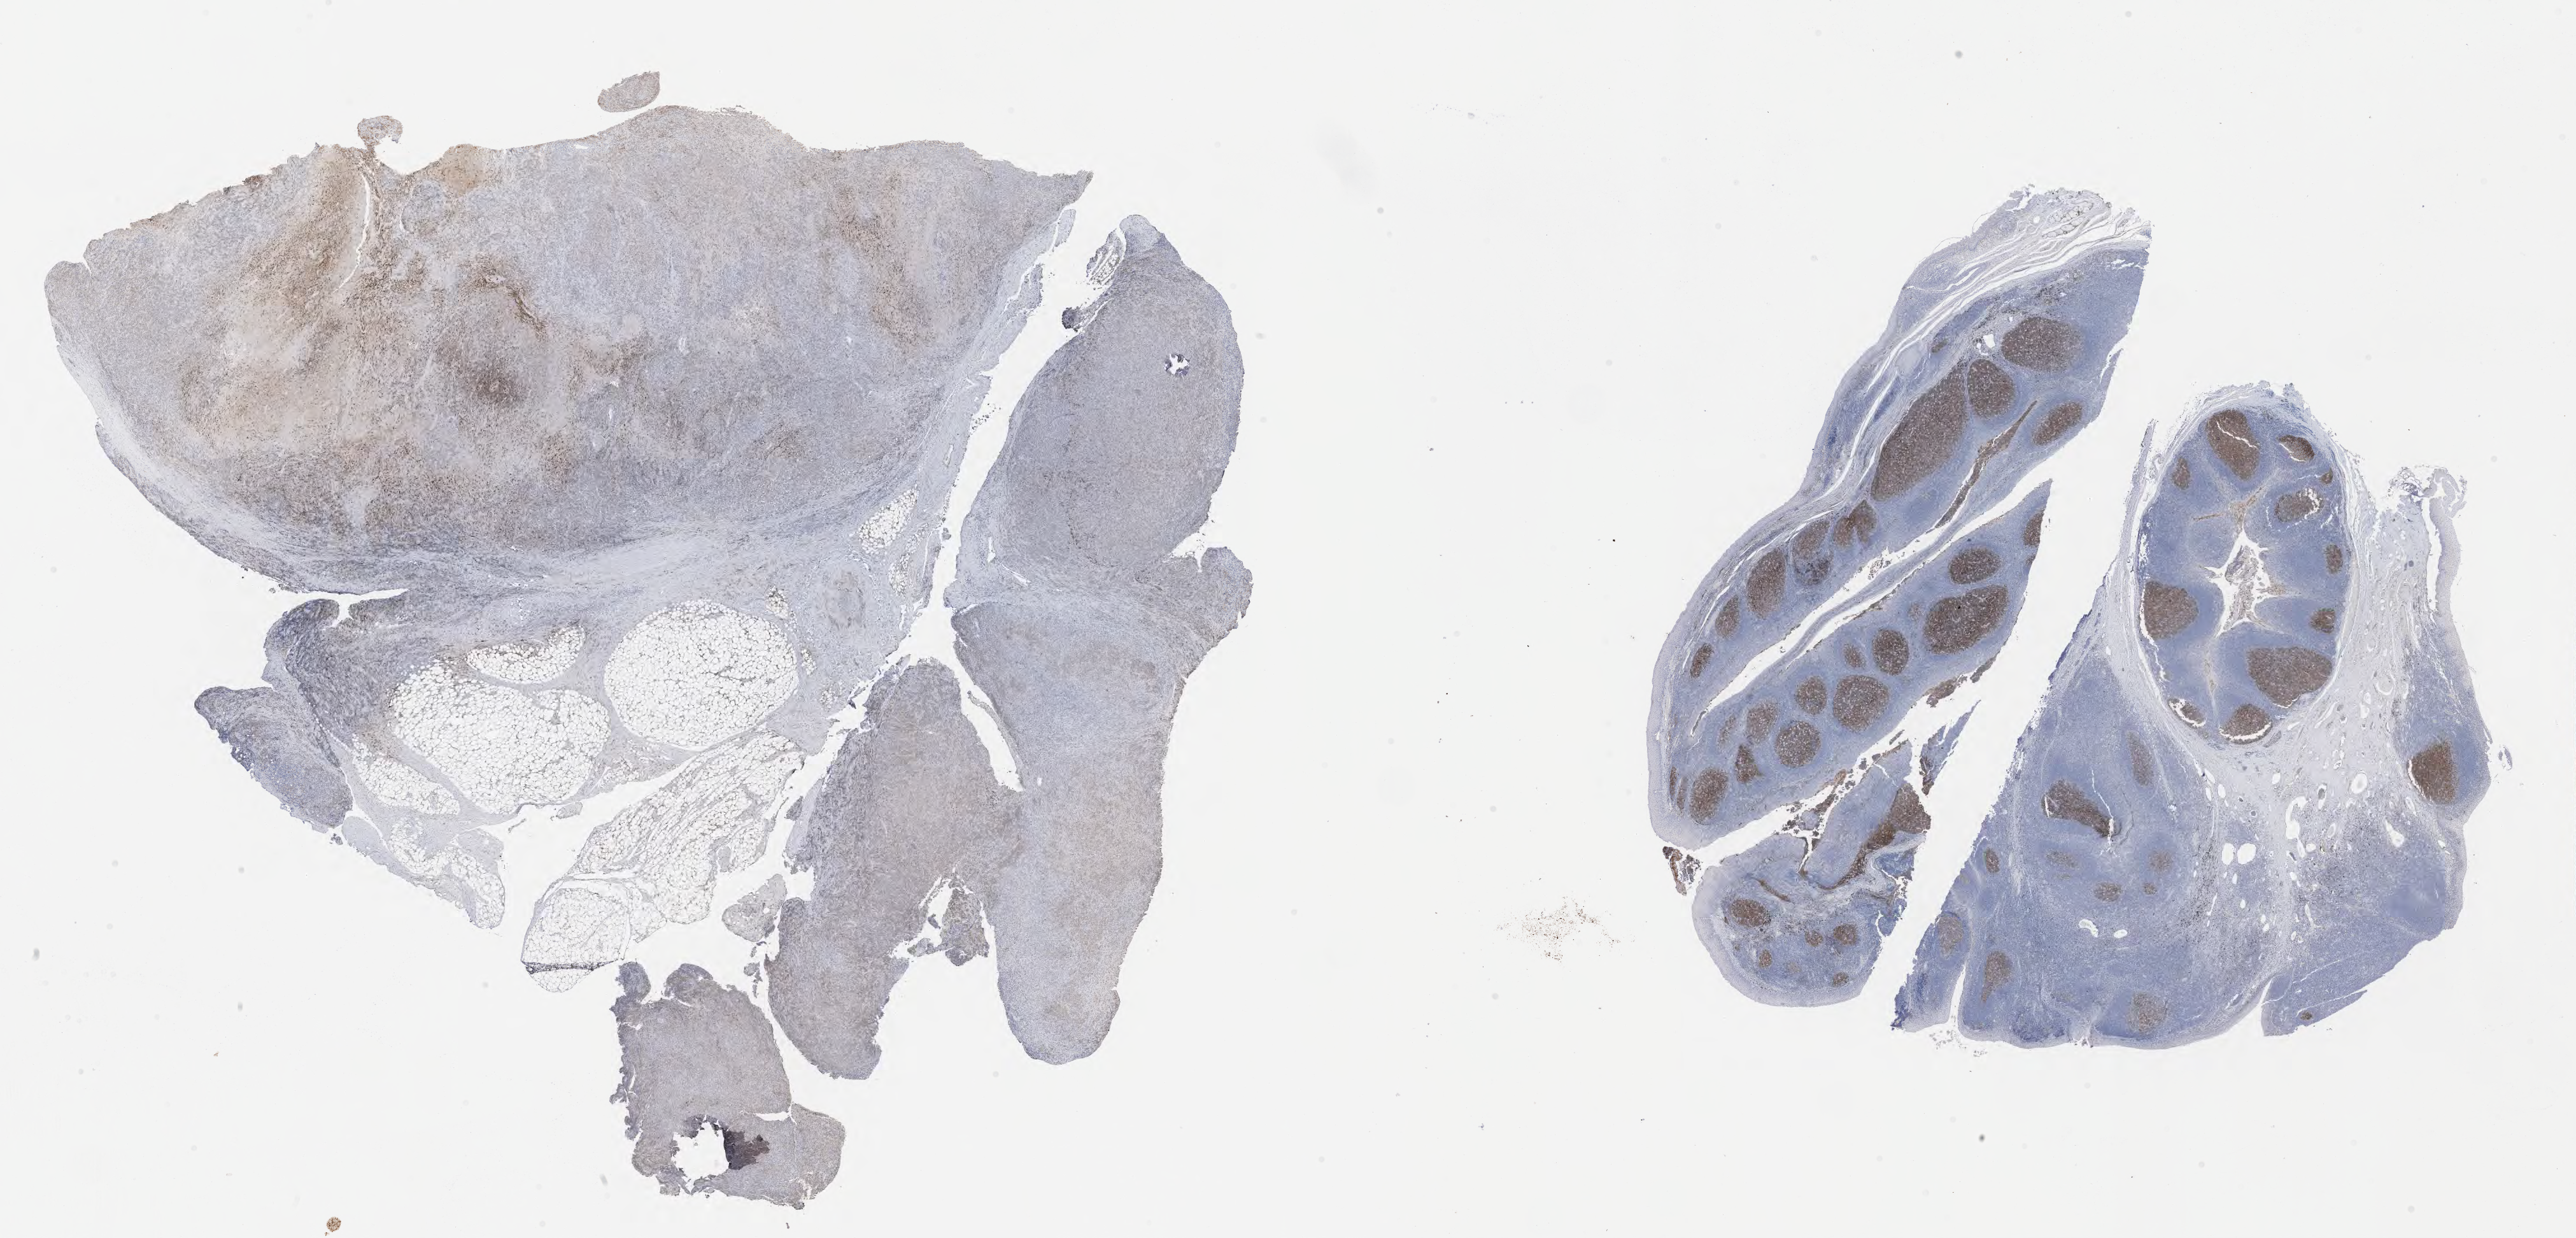
Immunohistochemistry (IHC) whole-slide image stained for CD10, a low-resolution overview of the entire scanned area, about 32.7 x 15.7 mm; tumor tissue. Patient female; 46 years old.
- diagnosis: Diffuse large B-cell lymphoma, NOS